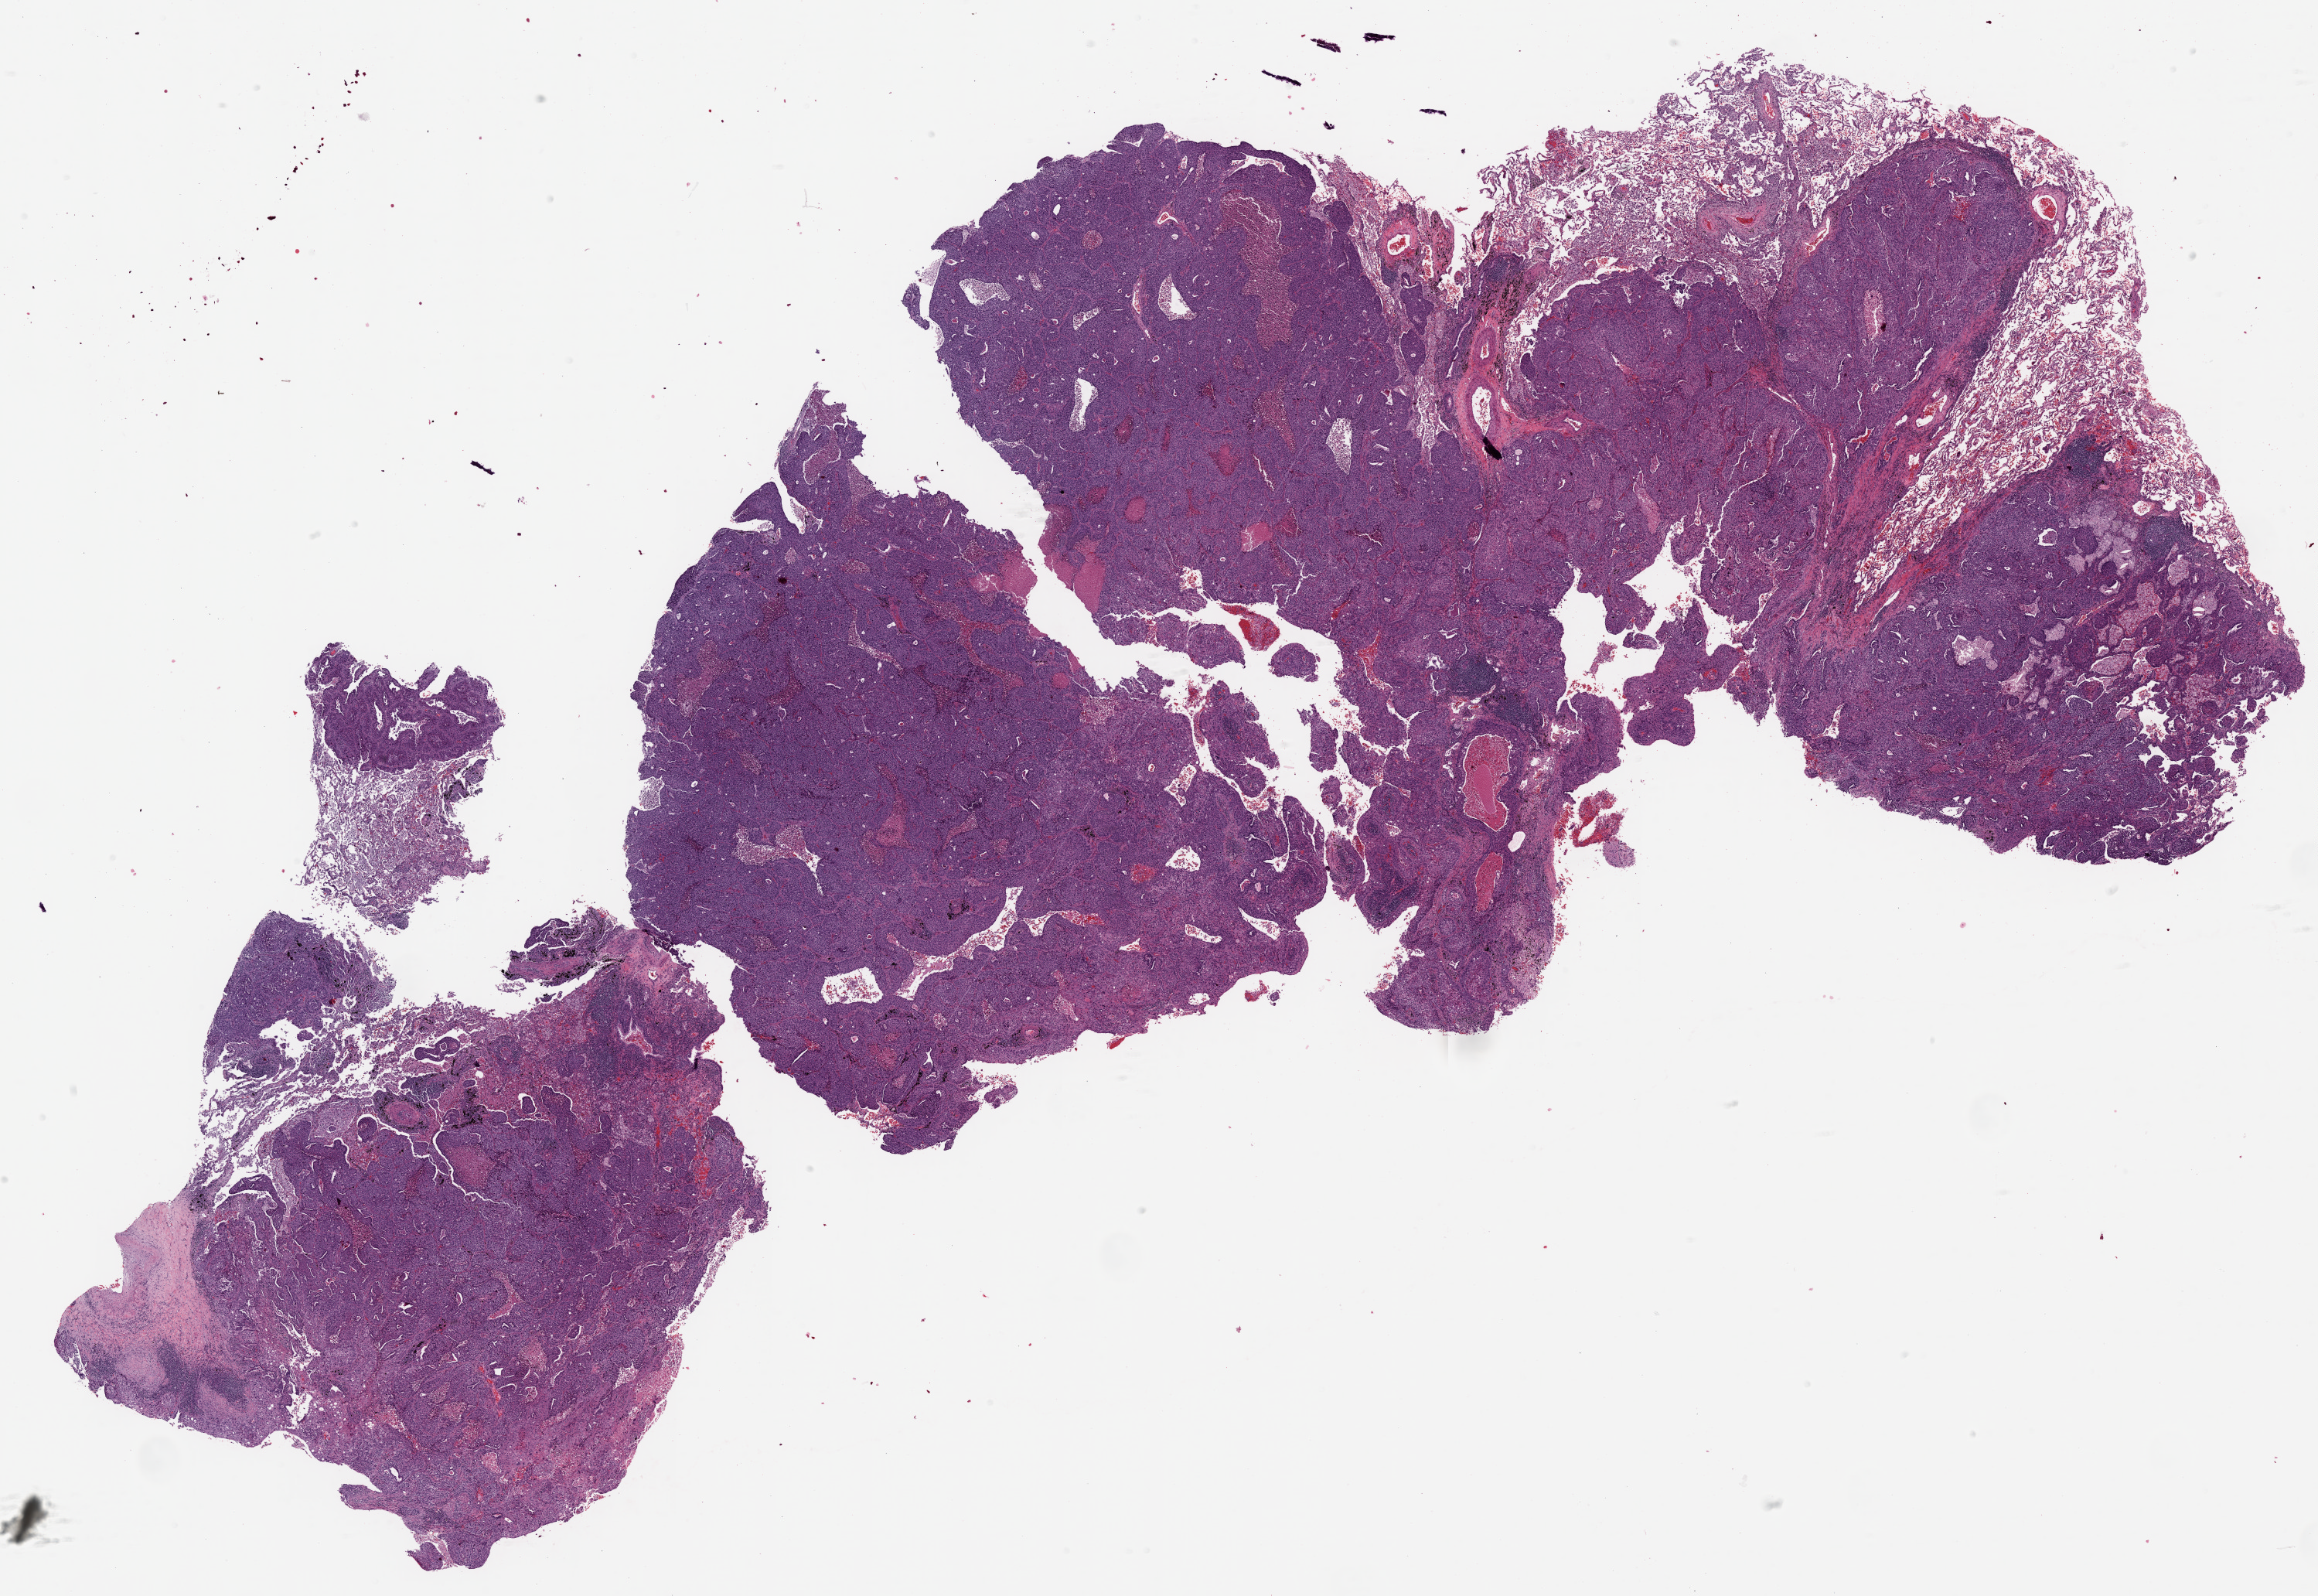
Hematoxylin and eosin (H&E) stained whole-slide image — whole scanned area (about 24.0 x 16.5 mm, from a 20x scan) shown as a low-resolution overview. Formalin-fixed paraffin-embedded (FFPE) diagnostic section. Lung, primary tumour sample. Patient: male, age at initial diagnosis 56 years.
• laterality: right
• AJCC pathologic stage: IIB (6th edition)
• diagnosis: Squamous cell carcinoma, NOS (lower lobe, lung)